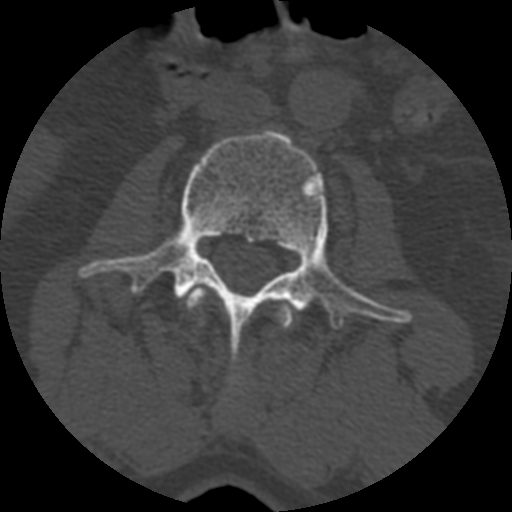
CT including the spine, one axial slice; reconstruction kernel STANDARD; 120 kVp; bone window (W 1800 / L 400 HU); 1.25 mm slice thickness; 512 × 512 image matrix, field of view 160 × 160 mm. Patient age 71 years. Case-level facts recorded for this patient, not image findings: primary cancer: prostate.
Outlined on this slice (semi-automatic segmentation, software-assisted and operator-edited):
- L2 vertebra: box from (x=187, y=288) to (x=292, y=386) px
- L3 vertebra: (x=79, y=131)–(x=406, y=379)